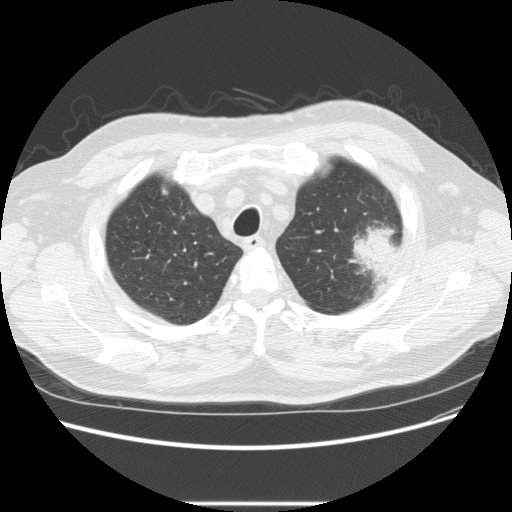
Axial slice from a low-dose chest CT screening exam. First (baseline) screen. Lung window (W 1500 / L -600 HU). 512 × 512 image matrix. Male participant, aged 73 years at enrolment. Former smoker at enrolment.
Expert reader's lesion annotation, bounding box (x1, y1, x2, y2) in pixels: (332, 216, 409, 284). The screening reader recorded 2 non-calcified nodules or masses ≥4 mm on this exam; which of them this box marks is not recorded.